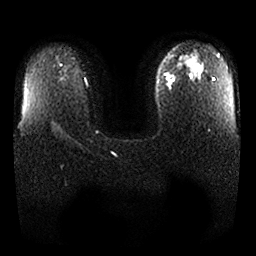
Breast MRI, one axial slice. Slice 18 of 25 in the series (ordered by position). Diffusion-weighted series; image 2 of 4 stored at this slice position (different b-values; order by instance number). 1.5 T. 4 mm slice thickness. 256 × 256 image matrix, field of view 340 × 340 mm. Female patient.
Outlined on this slice (expert manual segmentation):
- tumour on diffusion-weighted imaging: bounding box [x1, y1, x2, y2] px = [165, 75, 177, 91]